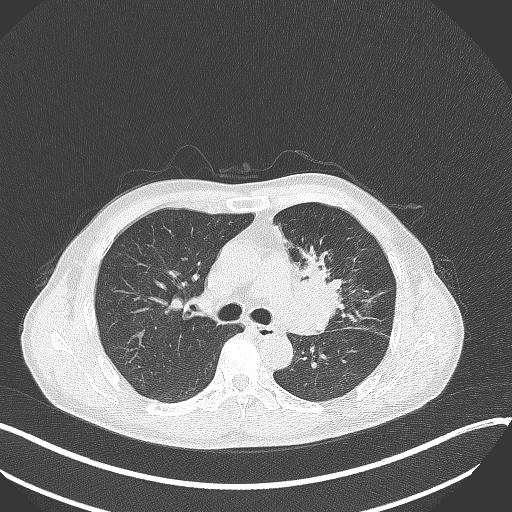
Chest CT, one axial slice. Position 212 of 411 along the scan axis. Reconstruction kernel B70f. 120 kVp. Lung window (W 1500 / L -600 HU). 1 mm slice thickness. 512 × 512 image matrix, field of view 400 × 400 mm. Male patient, age 56 years. Case-level facts recorded for this patient, not image findings: clinical TNM (as recorded): T2a N0 M0.
Annotated regions visible in this slice (rectangle marked by the reading radiologist):
- lung tumour (recorded histology: squamous cell carcinoma): bounding box <289,246,347,321> (left, top, right, bottom; pixels)